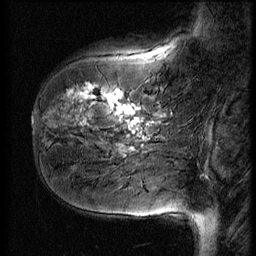
Breast MRI (dynamic contrast-enhanced), one sagittal slice. Slice 15 of 56 in the series (ordered by position). 3 images stored at this slice position (order not interpretable as contrast timing). 1.5 T. TE 4.2 ms, TR 9 ms. 2.5 mm slice thickness. 256 × 256 image matrix, field of view 180 × 180 mm. Female patient, age 51 years. Case-level facts recorded for this patient, not image findings: setting: breast cancer imaged before/during neoadjuvant chemotherapy; receptor status: HR-positive, HER2-negative.
Structures marked on this image (semi-automatically segmented with operator editing):
- analysis volume of interest (the breast-tissue region the enhancement analysis was run in; not a lesion): bounding box [x1, y1, x2, y2] px = [41, 58, 167, 161]
- tumour enhancement mask (voxels above the 140 % enhancement threshold inside the analysis volume of interest): [67, 84, 150, 153]